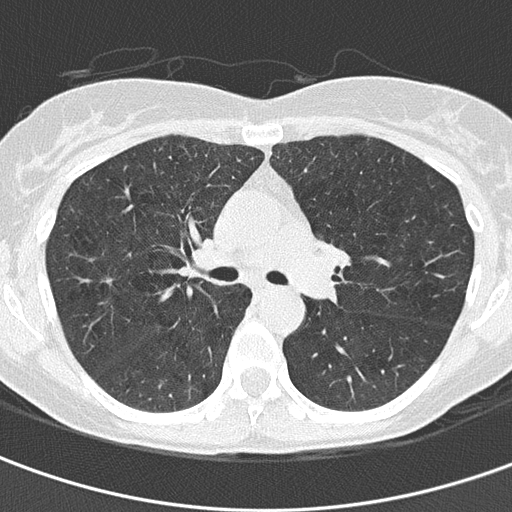
Low-dose screening chest CT, axial slice. Baseline annual screen. Lung window (W 1500 / L -600 HU). 2 mm slice thickness. 120 kVp. Slice 55 of 156 in the series. Female, age 59 years at enrolment. Current smoker at enrolment.
Lesion marked by an expert reader, bounding box [x1, y1, x2, y2] px = [89, 266, 127, 301]. No non-calcified nodule or mass ≥4 mm was recorded by the screening reader at this exam. Later outcome: lung cancer diagnosed 834 days after this screen (after the third annual screen) — bronchiolo-alveolar adenocarcinoma, NOS, right upper lobe, well differentiated (G1), stage IA (AJCC 6th edition), 4 mm at pathology.